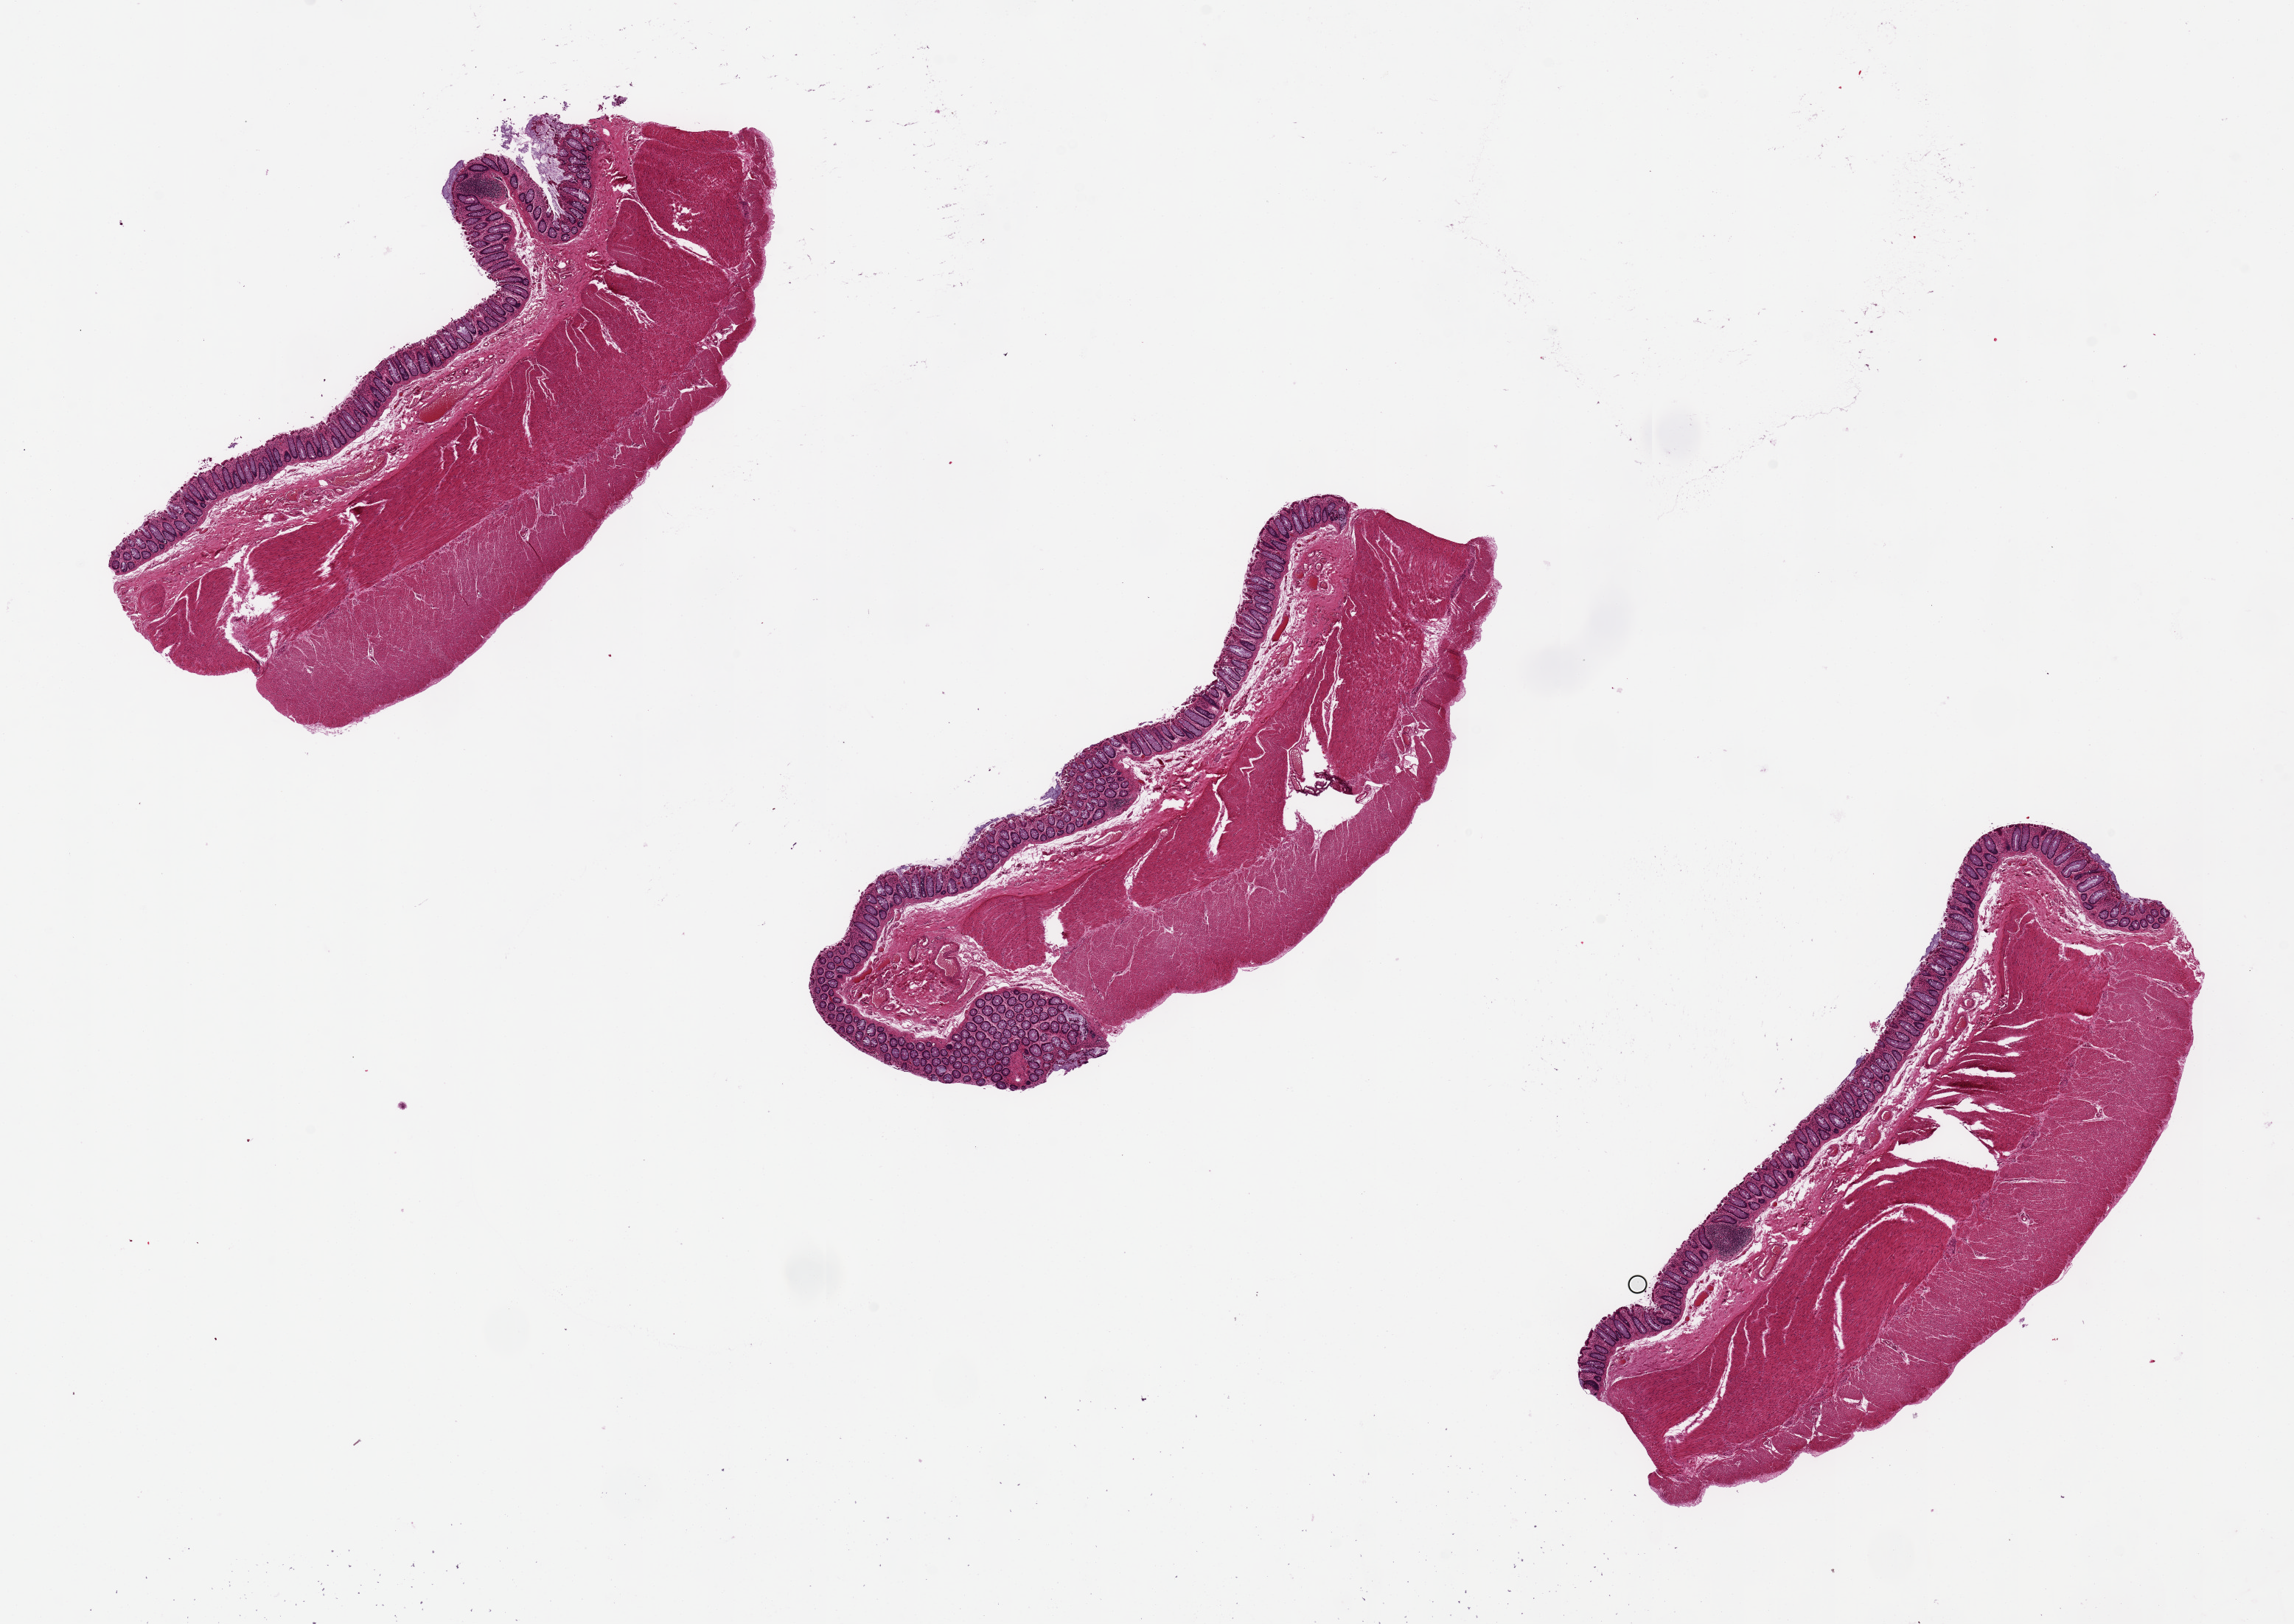
H&E whole-slide image, shown as a low-resolution overview of the whole scanned area (about 24.6 x 17.4 mm). PAXgene-fixed, paraffin-embedded tissue. Target tissue: transverse colon. Tissue donor sample. Donor: male.
Reviewer comment on this tissue sample: 3 pieces 2.6 mm thick, mucosa 0.4 mm; slight surface autolysis.